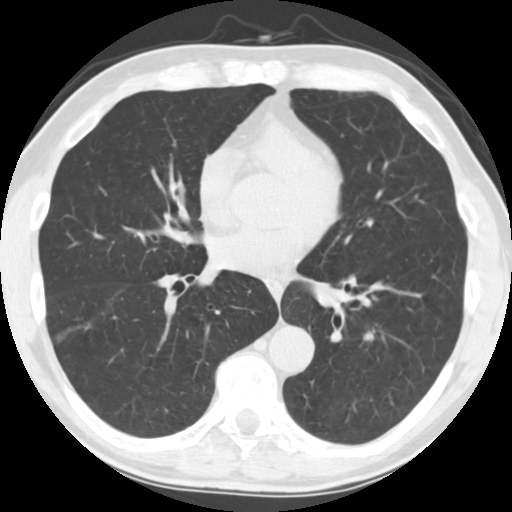
Axial slice from a low-dose chest CT screening exam; second annual screen; lung window (W 1500 / L -600 HU); 2.5 mm slice thickness; slice 107 of 245 in the series. Male participant, aged 64 years at enrolment. Current smoker at enrolment.
Expert reader's lesion annotation, box from (x=356, y=321) to (x=387, y=348) px. No non-calcified nodule or mass ≥4 mm was recorded by the screening reader at this exam. Official screen result: negative screen, no significant abnormalities.